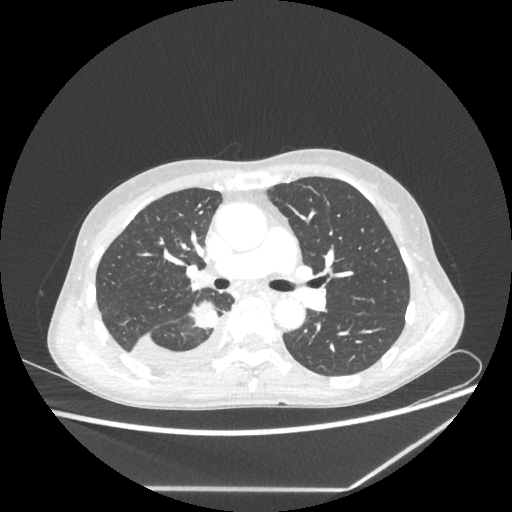
Chest CT, one axial slice. Position 139 of 237 along the scan axis. Lung window (W 1500 / L -600 HU). 512 × 512 image matrix, field of view 364 × 364 mm. Patient: female, 59 years. Case-level facts recorded for this patient, not image findings: clinical TNM (as recorded): T1c N1 M1.
Structures marked on this image (bounding box drawn by a radiologist):
- lung tumour (recorded histology: adenocarcinoma): bounding box (x1, y1, x2, y2) in pixels: (190, 300, 219, 332)